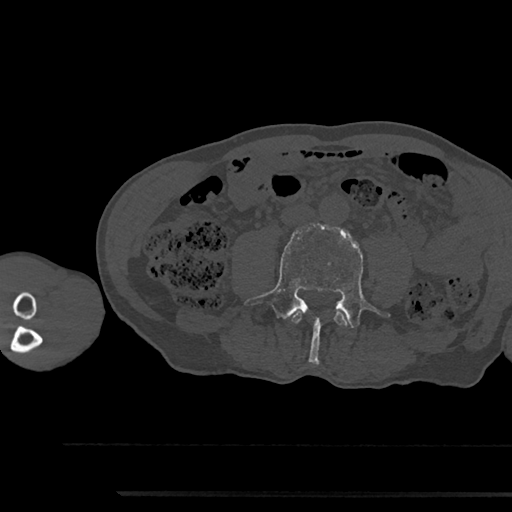
CT including the spine, one axial slice. Slice 428 of 797 in the series (ordered by position). Reconstruction kernel Br40s/3. Bone window (W 1800 / L 400 HU). 0.5 mm slice thickness. 512 × 512 image matrix. Male patient, age 79 years. From the clinical record (not read from this slice): primary cancer: prostate.
Annotated regions visible in this slice (semi-automatic segmentation, software-assisted and operator-edited):
- L3 vertebra: bounding box <292,312,348,326> (left, top, right, bottom; pixels)
- L4 vertebra: <244,224,390,364>